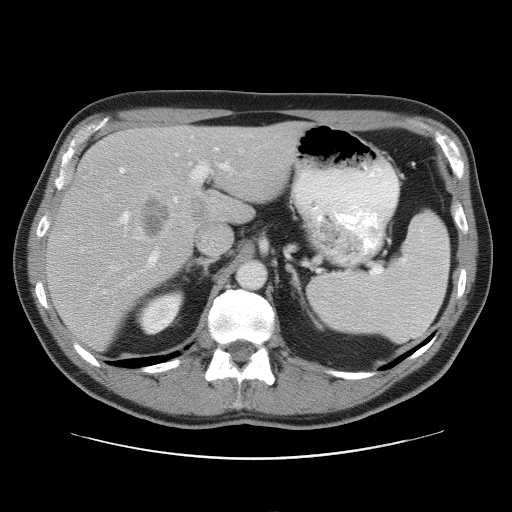
Contrast-enhanced abdominal CT, one axial slice. Slice 38 of 52 in the series (ordered by position). Reconstruction kernel STANDARD. Soft-tissue window (W 400 / L 40 HU). 5 mm slice thickness. 512 × 512 image matrix, field of view 393 × 393 mm. Male patient, age 70 years. Case-level facts recorded for this patient, not image findings: diagnosis: colorectal cancer liver metastases, imaged before liver resection; multiple liver metastases: yes; largest metastasis: 4 cm; chemotherapy before resection: yes.
Structures marked on this image (manually delineated by an expert):
- hepatic veins: bounding box <133,149,244,240> (left, top, right, bottom; pixels)
- liver: <47,122,303,349>
- planned liver remnant (the part of the liver to remain after resection): <107,122,303,209>
- portal vein (with intrahepatic branches): <102,147,232,294>
- liver metastasis: <191,198,207,224>
- liver metastasis: <141,200,171,237>